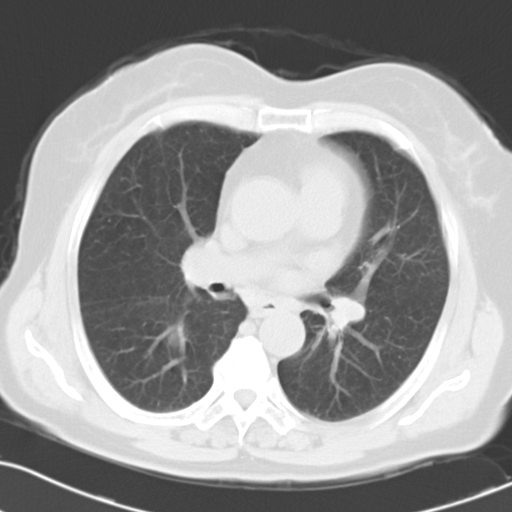
Chest CT, one axial slice. Slice 16 of 27 in the series (ordered by position). Lung window (W 1500 / L -600 HU). 10 mm slice thickness. 512 × 512 image matrix. Patient: female, 70 years. Case-level facts recorded for this patient, not image findings: clinical TNM (as recorded): T1c N3 M0; histopathological grade: G3.
Annotated regions visible in this slice (rectangle marked by the reading radiologist):
- lung tumour (recorded histology: small cell carcinoma): bounding box [x1, y1, x2, y2] px = [157, 313, 187, 355]